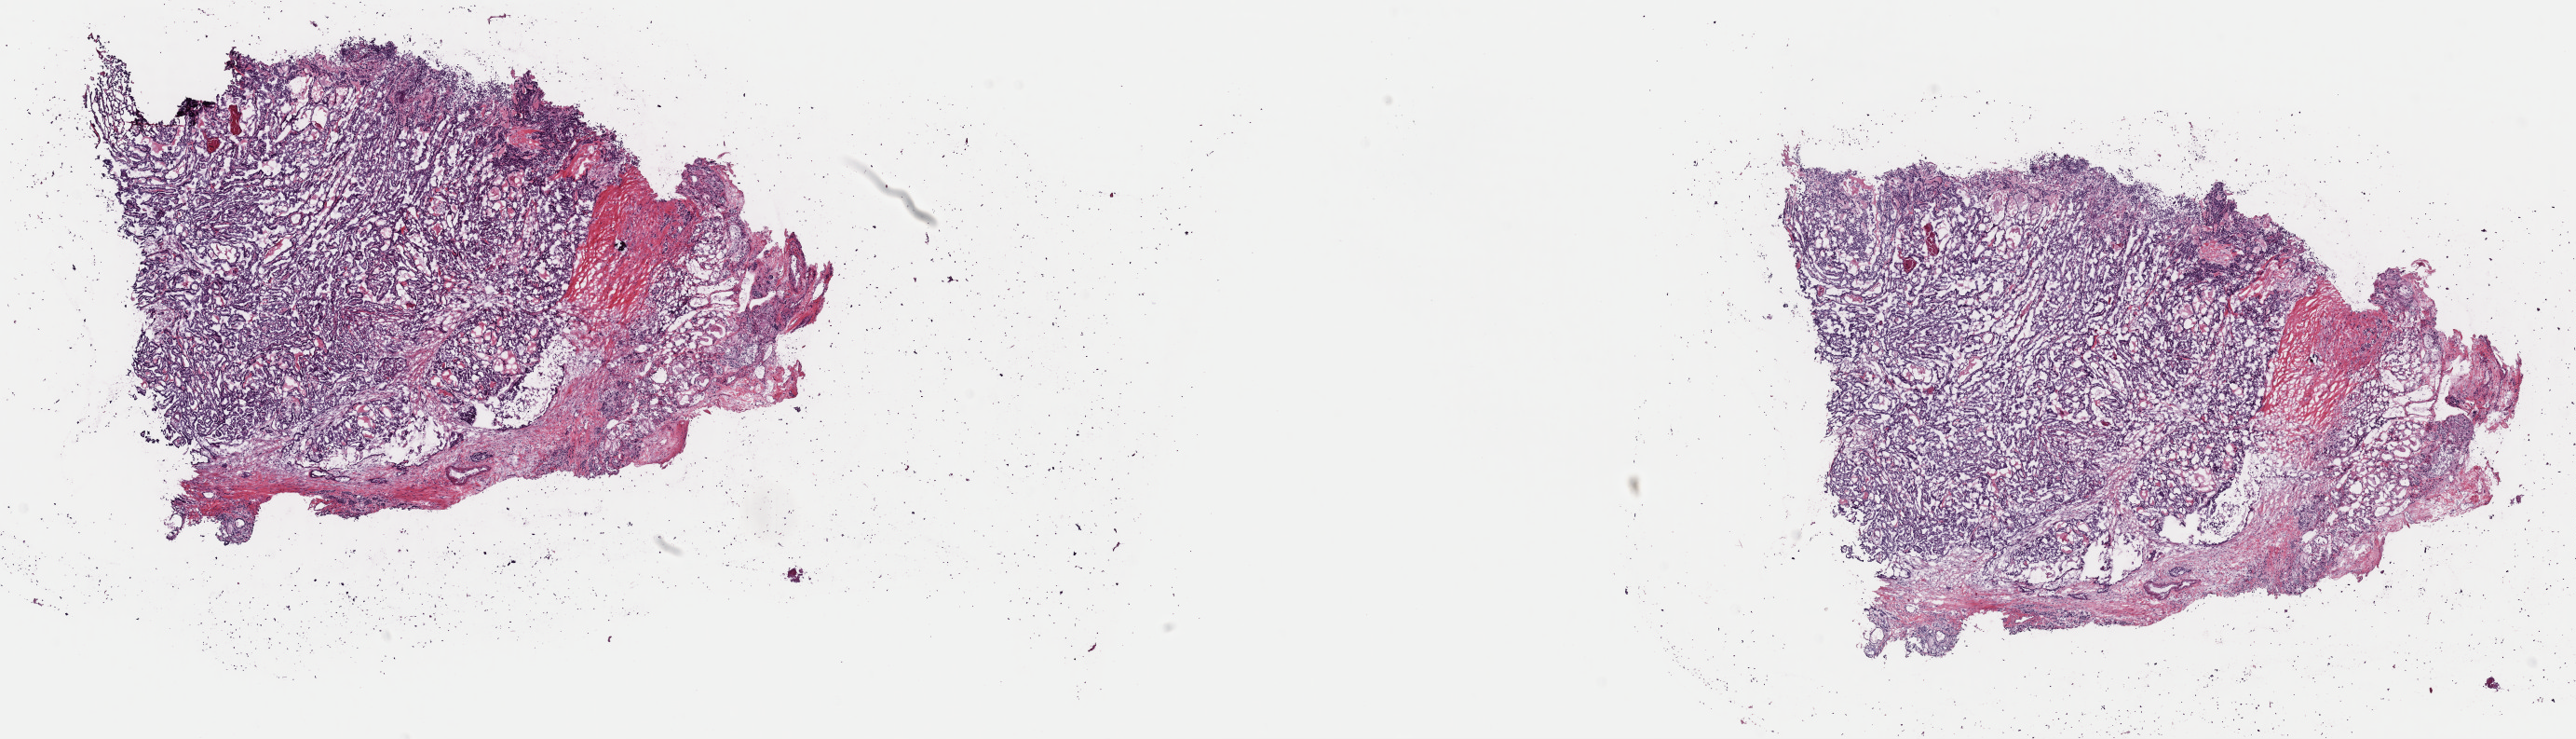
Digitized H&E-stained tissue section (whole slide) — a low-resolution overview of the entire scanned area, about 21.9 x 6.3 mm; frozen section from the top of the tissue portion; sample: primary tumour, thyroid. Female patient; age at initial diagnosis 38 years. Pathologist review of this section (percent, as recorded): tumour cells 65%, tumour nuclei 65%, normal cells 5%, stromal cells 30%, necrosis 0%. Infiltration values recorded for this section: lymphocyte infiltration 5%, monocyte infiltration 2%, neutrophil infiltration 2%.
* pathologic diagnosis: Papillary adenocarcinoma, NOS (thyroid gland)
* AJCC pathologic stage: I
* TNM: T1b N0 M0